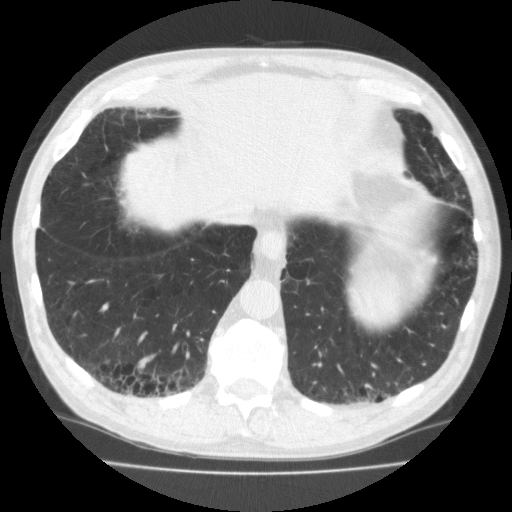
Low-dose screening chest CT, one axial slice; position 54 of 195 along the scan axis; reconstruction kernel FC10; 120 kVp; lung window (W 1500 / L -600 HU); 2 mm slice thickness; 512 × 512 image matrix, field of view 350 × 350 mm.
Annotated regions visible in this slice (manually delineated by an expert):
- lesion 1 (tumor, lower lobe of right lung): bounding box [x1, y1, x2, y2] px = [137, 360, 154, 375]